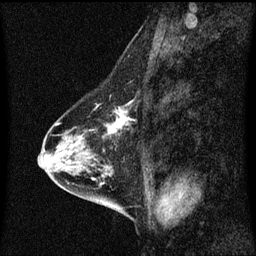
Breast MRI (dynamic contrast-enhanced), one sagittal slice. Position 26 of 60 along the scan axis. Dynamic contrast-enhanced series, image 2 of 3 at this slice position (ordered by acquisition). 1.5 T. TE 4.2 ms, TR 8.4 ms. 2 mm slice thickness. 256 × 256 image matrix, field of view 200 × 200 mm. Patient: female, 58 years.
Structures marked on this image (semi-automatically segmented with operator editing):
- analysis volume of interest (the breast-tissue region the enhancement analysis was run in; not a lesion): bounding box (x1, y1, x2, y2) in pixels: (86, 92, 139, 143)
- tumour enhancement mask (voxels above the 70 % enhancement threshold inside the analysis volume of interest): (92, 102, 133, 135)